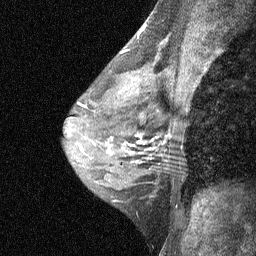
Breast MRI (dynamic contrast-enhanced), one sagittal slice; position 38 of 64 along the scan axis; dynamic contrast-enhanced study with each time point stored as its own series, time point 3 of 4 at this slice position (ordered by acquisition time); 1.5 T; TE 4.8 ms, TR 27 ms; 256 × 256 image matrix. Patient: female, 44 years. Case-level facts recorded for this patient, not image findings: setting: breast cancer imaged before/during neoadjuvant chemotherapy; receptor status: HR-positive, HER2-negative.
Annotated regions visible in this slice (semi-automatically segmented with operator editing):
- analysis volume of interest (the breast-tissue region the enhancement analysis was run in; not a lesion): bounding box <115,117,185,188> (left, top, right, bottom; pixels)
- tumour enhancement mask (voxels above the 90 % enhancement threshold inside the analysis volume of interest): <124,143,151,149>